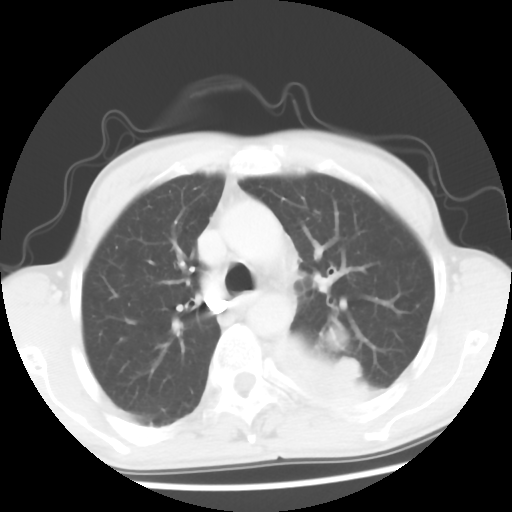
Chest CT, one axial slice; position 40 of 56 along the scan axis; 120 kVp; lung window (W 1500 / L -600 HU); 5 mm slice thickness; 512 × 512 image matrix, field of view 318 × 318 mm. Male patient, age 60 years. From the clinical record (not read from this slice): clinical TNM (as recorded): T4 N0 M0.
Outlined on this slice (rectangle marked by the reading radiologist):
- lung tumour (recorded histology: squamous cell carcinoma): box from (x=269, y=318) to (x=392, y=419) px